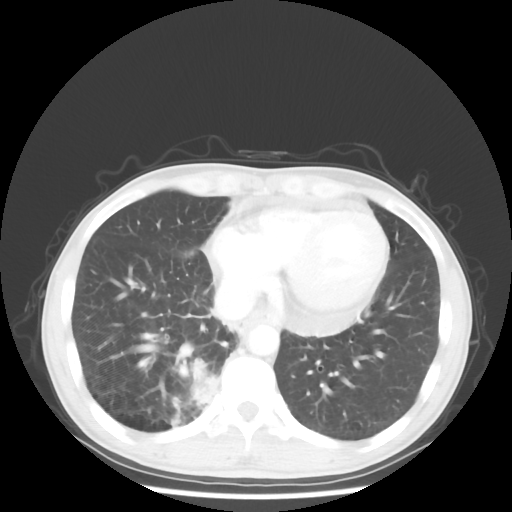
Chest CT, one axial slice; slice 15 of 58 in the series (ordered by position); reconstruction kernel STANDARD; lung window (W 1500 / L -600 HU); 5 mm slice thickness; 512 × 512 image matrix, field of view 360 × 360 mm. Male patient, age 56 years. From the clinical record (not read from this slice): clinical TNM (as recorded): T2 N1 M1; histopathological grade: G1.
Annotated regions visible in this slice (bounding box drawn by a radiologist):
- lung tumour (recorded histology: adenocarcinoma): bounding box [x1, y1, x2, y2] px = [186, 353, 220, 412]